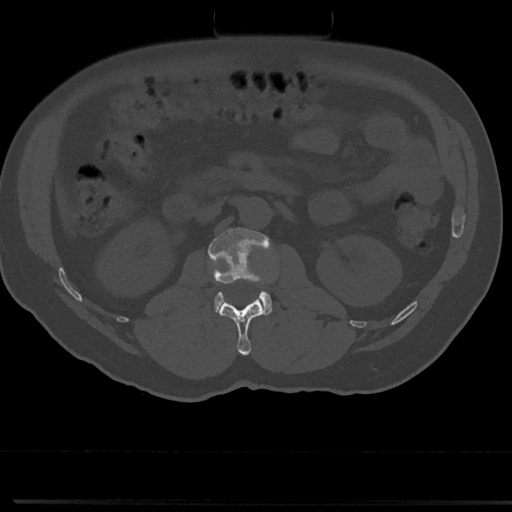
CT including the spine, one axial slice; position 46 of 817 along the scan axis; reconstruction kernel Br40s/3; 120 kVp; bone window (W 1800 / L 400 HU); 0.5 mm slice thickness; 512 × 512 image matrix, field of view 355 × 355 mm. Patient: male, 61 years. Case-level facts recorded for this patient, not image findings: primary cancer: prostate.
Outlined on this slice (semi-automatic segmentation, software-assisted and operator-edited):
- L1 vertebra: box from (x=219, y=299) to (x=264, y=355) px
- L2 vertebra: (x=208, y=227)–(x=272, y=316)